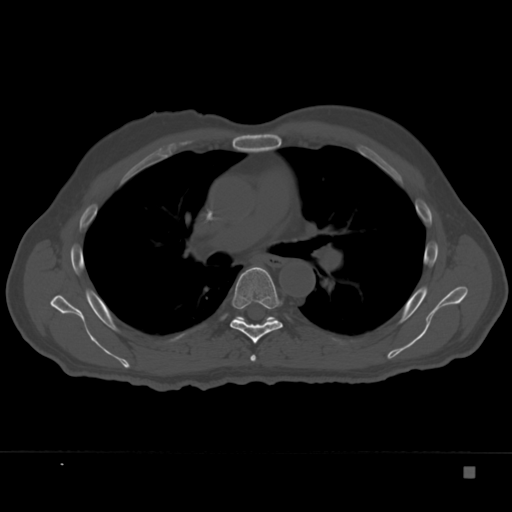
CT including the spine, one axial slice; position 239 of 332 along the scan axis; reconstruction kernel Br40s; 120 kVp; bone window (W 1800 / L 400 HU); 512 × 512 image matrix. Male patient, age 72 years. From the clinical record (not read from this slice): primary cancer: skeletal.
Outlined on this slice (semi-automatically segmented with operator editing):
- T5 vertebra: bounding box [x1, y1, x2, y2] px = [250, 355, 256, 362]
- T6 vertebra: [230, 267, 283, 344]